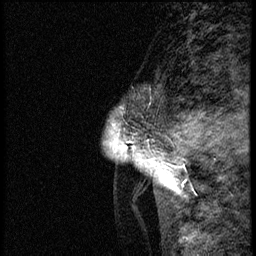
Breast MRI (dynamic contrast-enhanced), one sagittal slice; slice 1 of 68 in the series (ordered by position); dynamic contrast-enhanced study with each time point stored as its own series, time point 2 of 3 at this slice position (early post-contrast, ordered by acquisition time); 1.5 T; TE 4.2 ms, TR 17.6 ms; 256 × 256 image matrix, field of view 200 × 200 mm. Patient: female, 52 years. From the clinical record (not read from this slice): setting: breast cancer imaged before/during neoadjuvant chemotherapy; receptor status: HER2-positive.
Annotated regions visible in this slice (semi-automatic segmentation, software-assisted and operator-edited):
- analysis volume of interest (the breast-tissue region the enhancement analysis was run in; not a lesion): bounding box (x1, y1, x2, y2) in pixels: (106, 72, 176, 184)
- tumour enhancement mask (voxels above the 100 % enhancement threshold inside the analysis volume of interest): (107, 106, 176, 176)